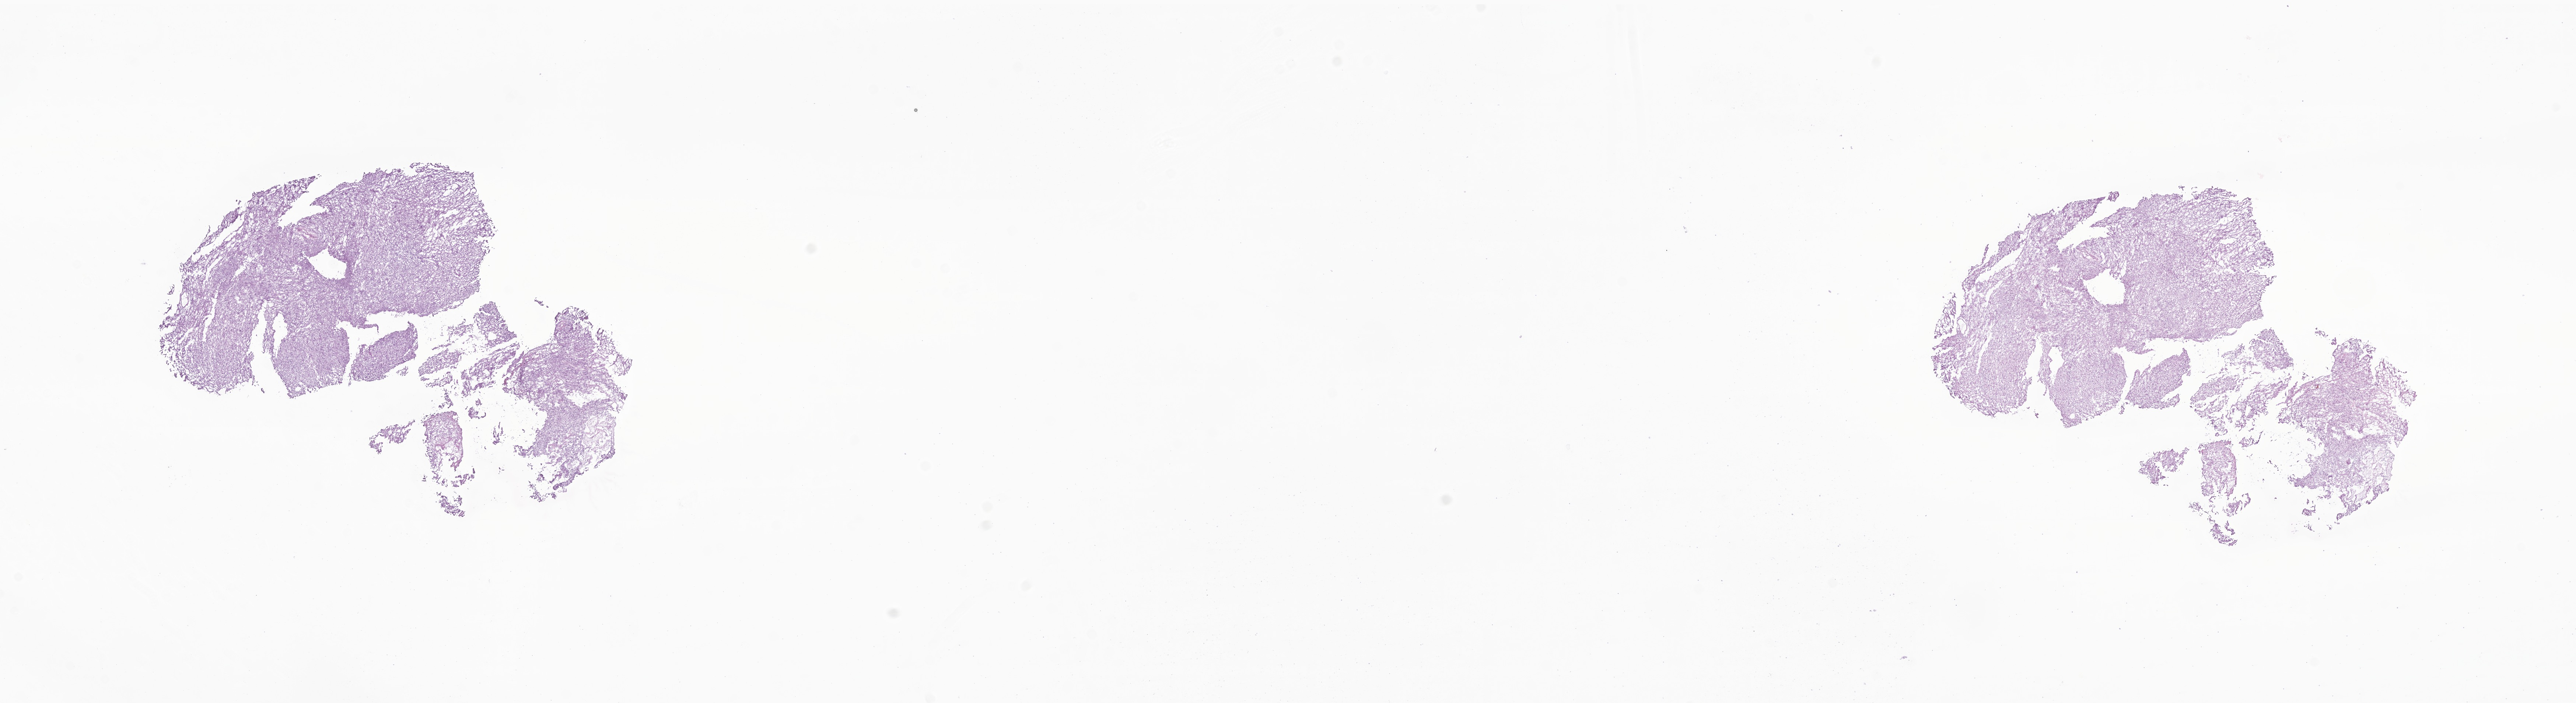
Haematoxylin and eosin whole-slide image of tumor tissue from the spinal cord, shown as a low-resolution overview of the whole scanned area (about 29.5 x 8.0 mm). Frozen section (OCT-embedded). Patient: male, age 213 months (17 years 9 months).
Diagnosis: Soft tissue tumor, benign.